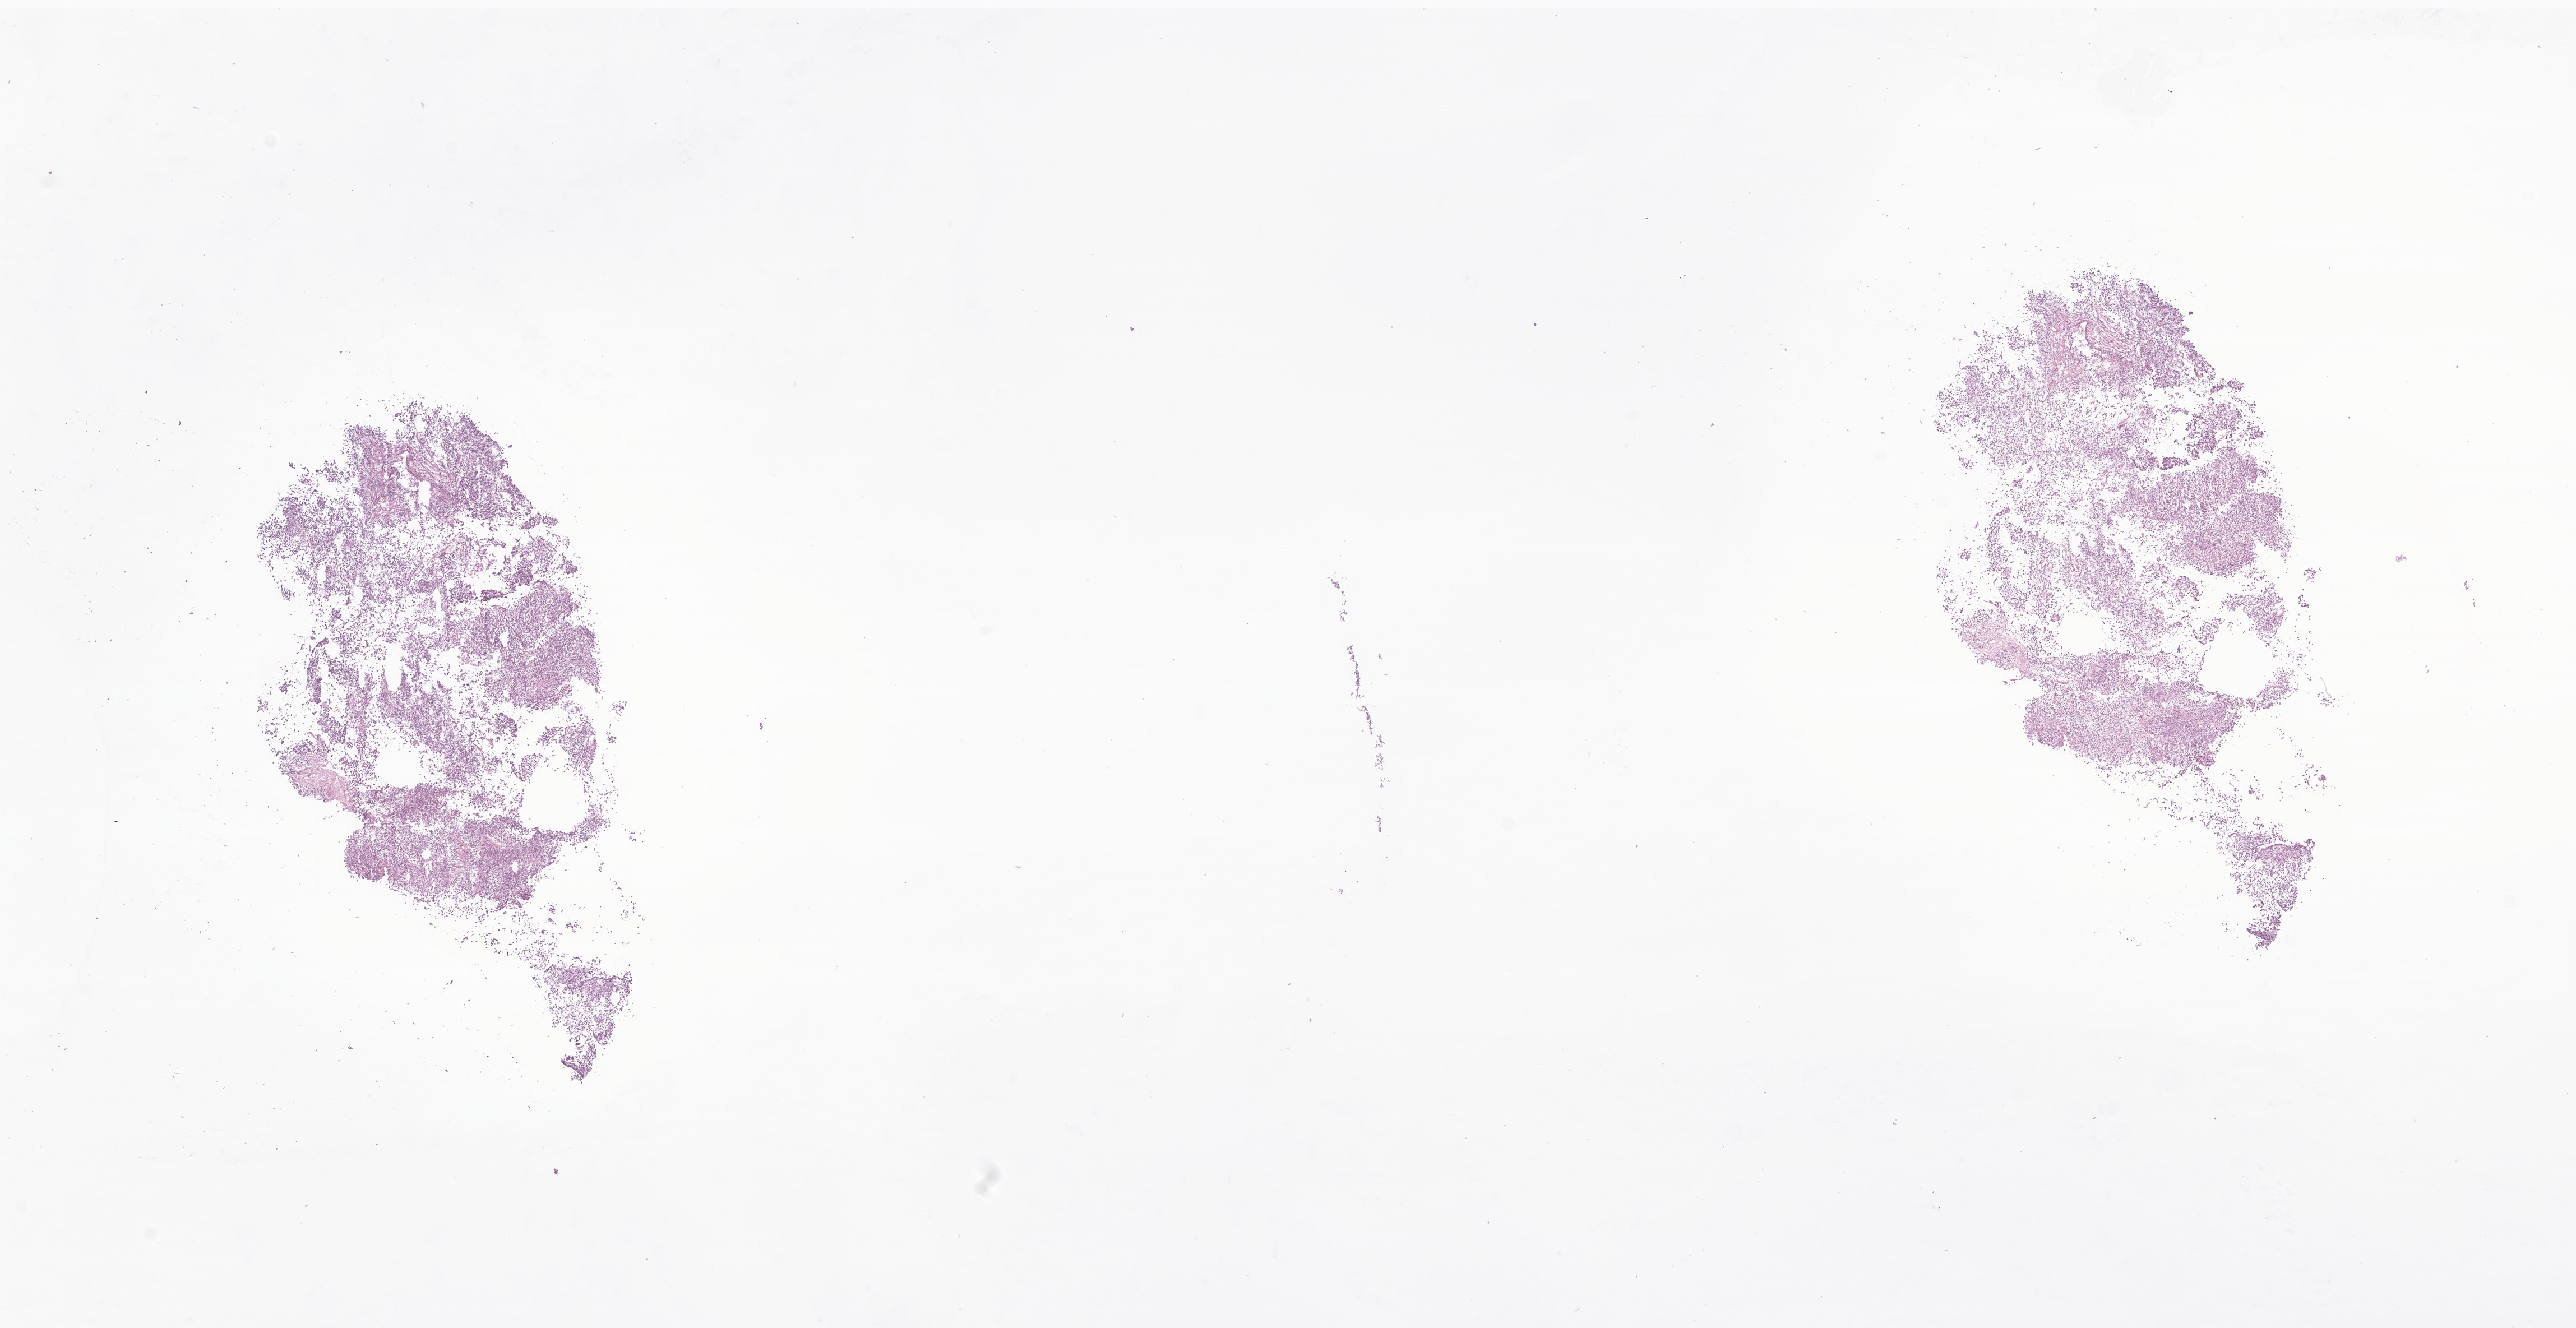
H&E whole-slide image of tumor tissue from the brain, a low-resolution overview of the entire scanned area, about 19.4 x 10.0 mm. Cryosection (OCT / tissue freezing medium). Patient male; age 631 days (about 1.7 years).
Recorded diagnosis: Atypical teratoid/rhabdoid tumor.